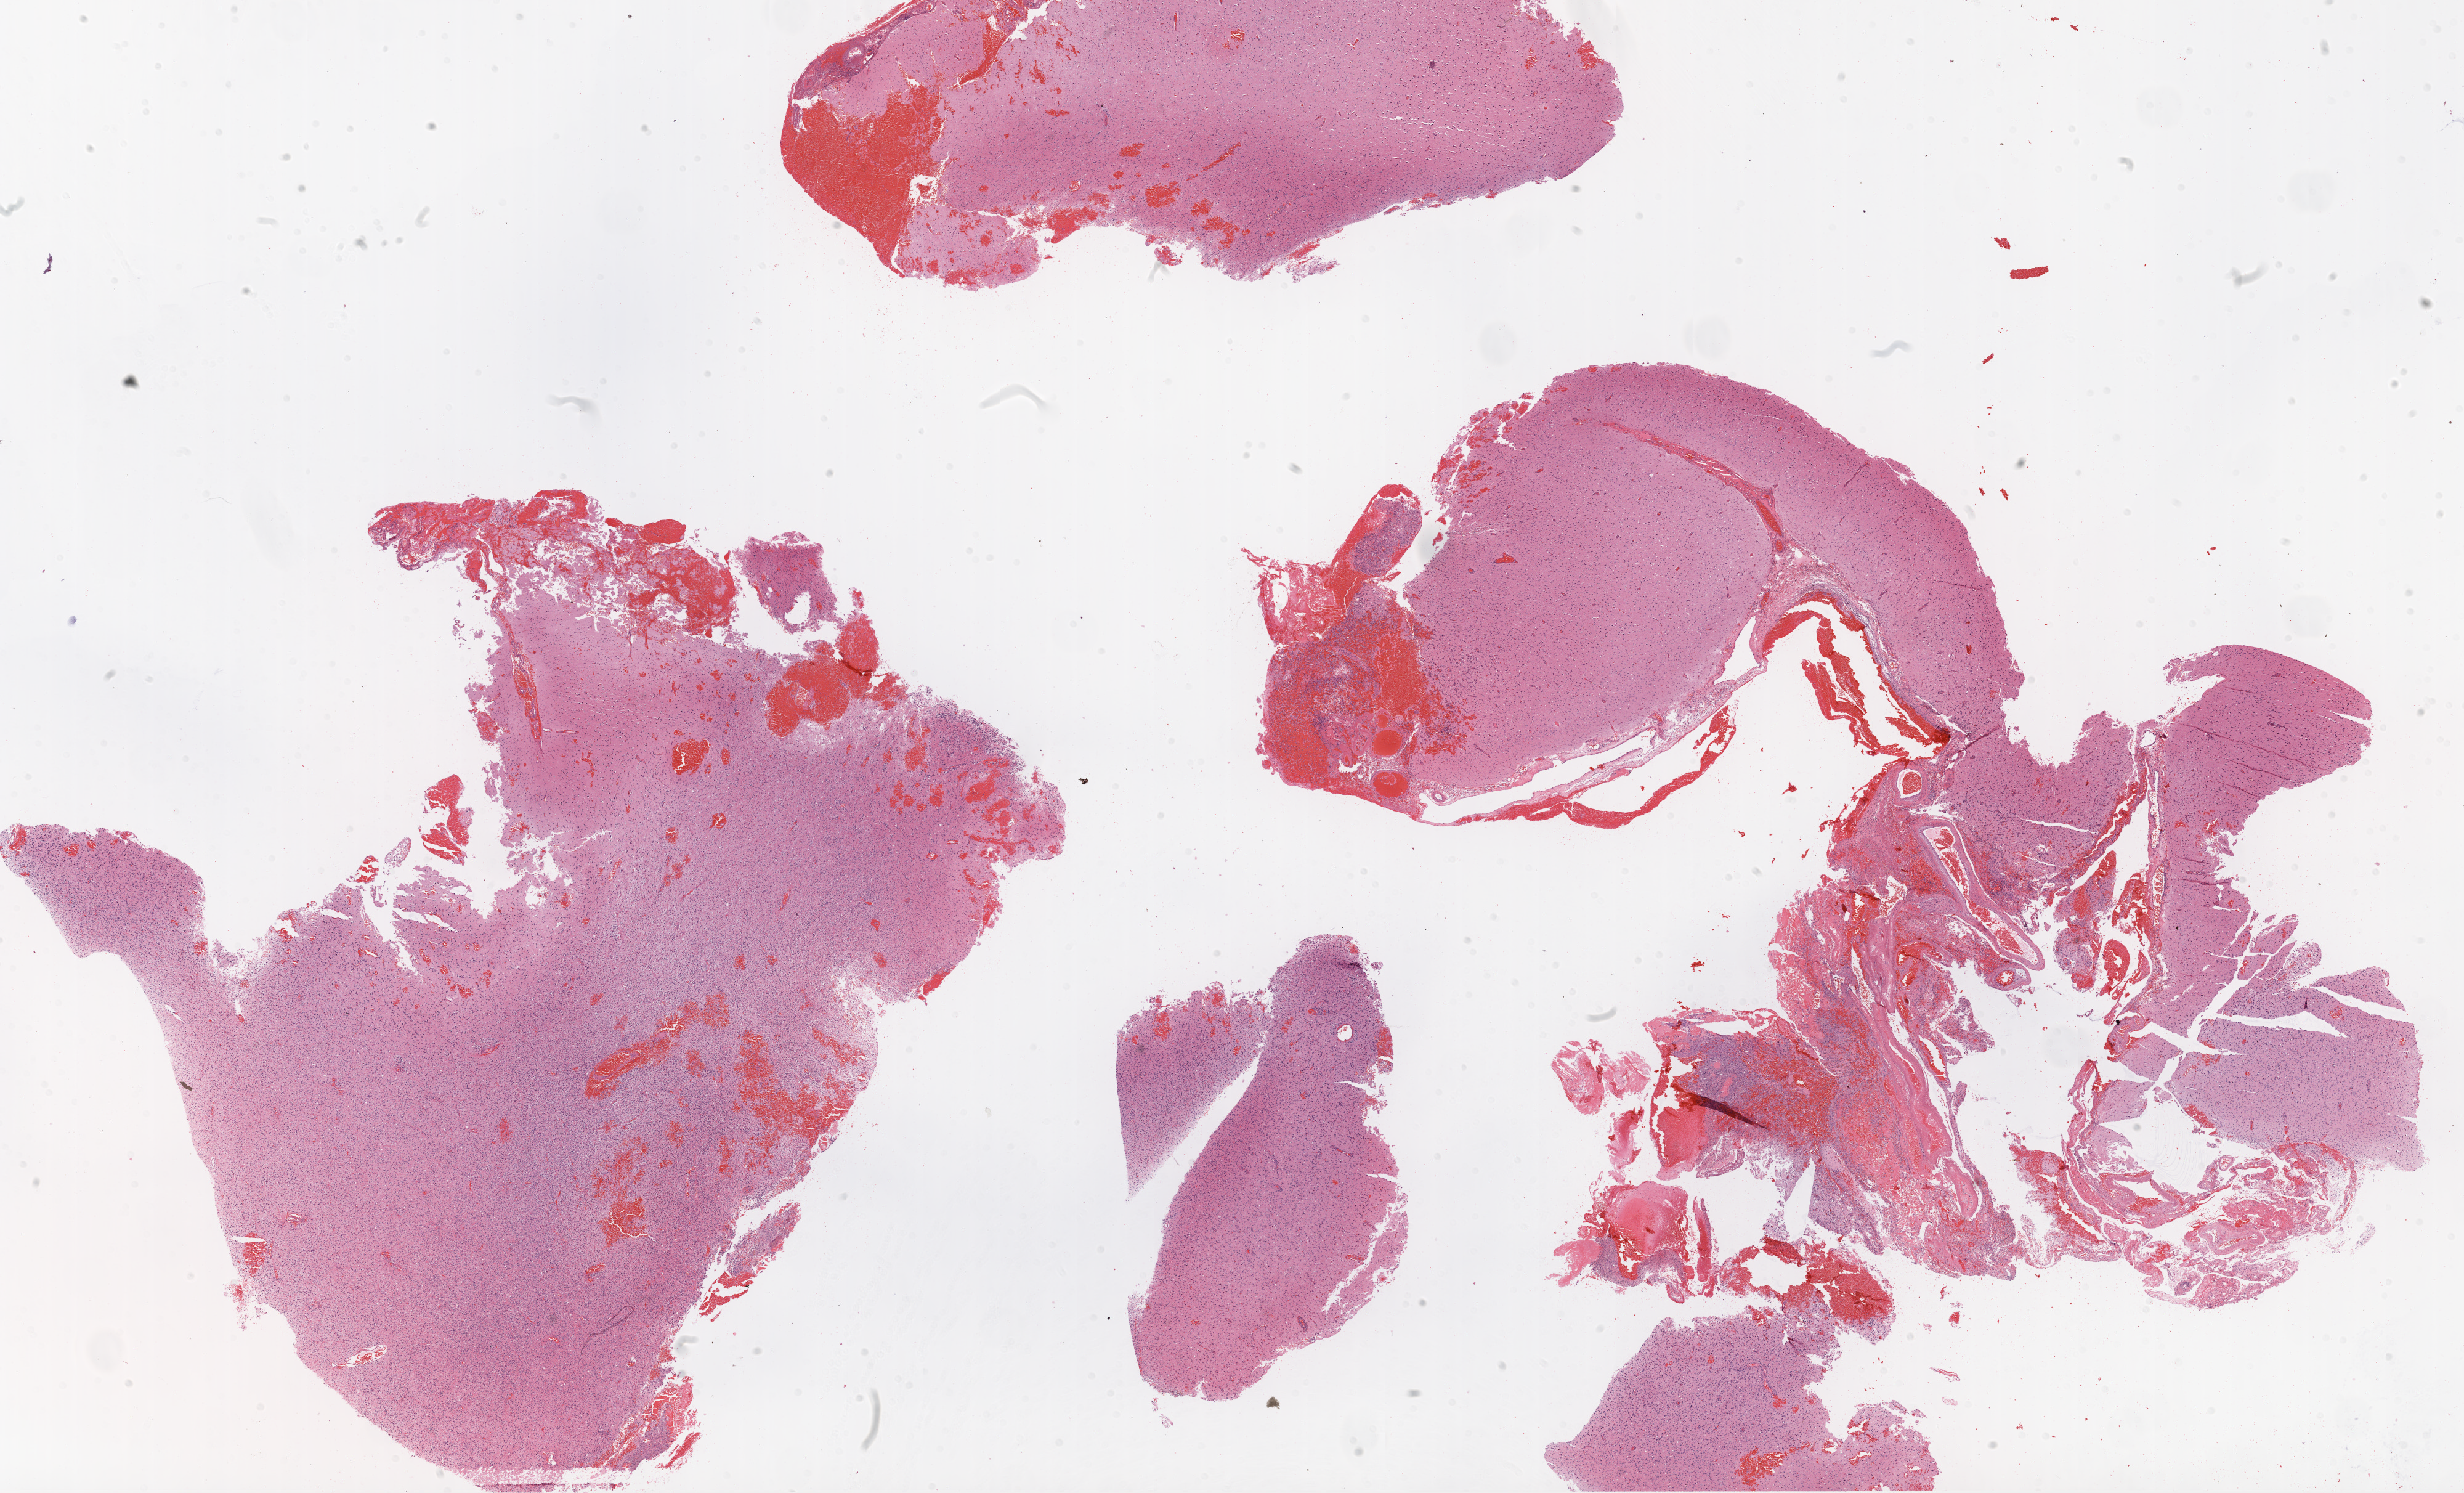
Digitized H&E-stained tissue section (whole slide) — whole scanned area (about 32.1 x 19.4 mm, slide scanned at 20x) shown as a low-resolution overview; formalin-fixed paraffin-embedded (FFPE) diagnostic section; primary tumour sample from the brain. Male, age 38 years at initial diagnosis.
Diagnosis: Glioblastoma.